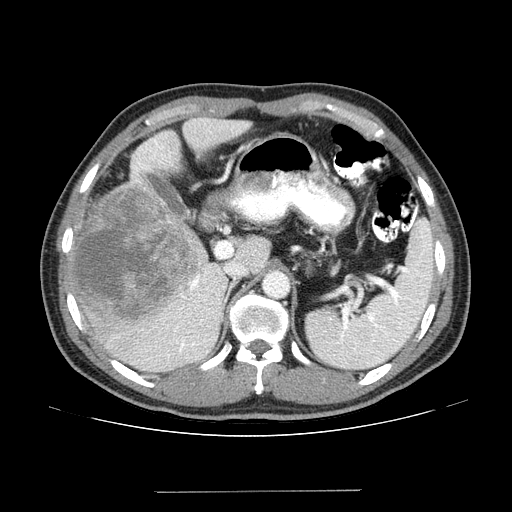
Contrast-enhanced abdominal CT (liver protocol), one axial slice; slice 90 of 131 in the series (ordered by position); reconstruction kernel STANDARD; 100 kVp; one of 2 acquisitions stored at this slice position; soft-tissue window (W 400 / L 40 HU); 512 × 512 image matrix, field of view 380 × 380 mm. Case-level facts recorded for this patient, not image findings: diagnosis: hepatocellular carcinoma (patient treated with transarterial chemoembolisation; whether this scan precedes or follows treatment is not stated here); TNM stage (as recorded): Stage-I; Child-Pugh class: A.
Outlined on this slice (semi-automatic segmentation, software-assisted and operator-edited):
- liver parenchyma outside the tumour (the mass and vessels are separate outlines, so this box may not span the whole liver): bounding box (x1, y1, x2, y2) in pixels: (66, 116, 252, 372)
- mass: (66, 183, 206, 328)
- liver vessels: (135, 140, 208, 357)